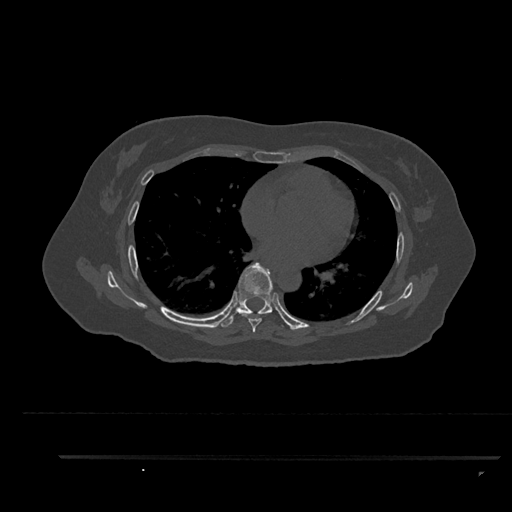
CT including the spine, one axial slice. Position 531 of 797 along the scan axis. Reconstruction kernel Br40s/3. Bone window (W 1800 / L 400 HU). 512 × 512 image matrix, field of view 408 × 408 mm. Female patient, age 44 years. From the clinical record (not read from this slice): primary cancer: renal; vertebrae with lytic lesions (as recorded): L1.
Outlined on this slice (semi-automatically segmented with operator editing):
- T6 vertebra: bounding box [x1, y1, x2, y2] px = [242, 313, 268, 333]
- T7 vertebra: [220, 262, 289, 328]